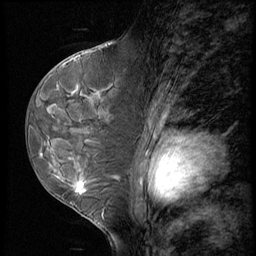
Breast MRI (dynamic contrast-enhanced), one sagittal slice; position 34 of 60 along the scan axis; 3 images stored at this slice position (order not interpretable as contrast timing); 1.5 T; TE 4.2 ms, TR 8.9 ms; 256 × 256 image matrix, field of view 200 × 200 mm. Patient: female, 50 years. From the clinical record (not read from this slice): setting: breast cancer imaged before/during neoadjuvant chemotherapy; receptor status: HR-positive, HER2-negative.
Outlined on this slice (semi-automatically segmented with operator editing):
- analysis volume of interest (the breast-tissue region the enhancement analysis was run in; not a lesion): bounding box [x1, y1, x2, y2] px = [38, 102, 118, 213]
- tumour enhancement mask (voxels above the 140 % enhancement threshold inside the analysis volume of interest): [77, 182, 86, 193]